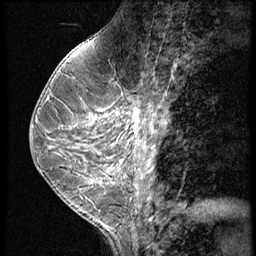
Breast MRI (dynamic contrast-enhanced), one sagittal slice; position 26 of 60 along the scan axis; 3 images stored at this slice position (order not interpretable as contrast timing); 1.5 T; TE 4.2 ms, TR 9 ms; 2.5 mm slice thickness; 256 × 256 image matrix, field of view 180 × 180 mm. Female patient, age 38 years. From the clinical record (not read from this slice): setting: breast cancer imaged before/during neoadjuvant chemotherapy; receptor status: triple-negative.
Annotated regions visible in this slice (semi-automatically segmented with operator editing):
- analysis volume of interest (the breast-tissue region the enhancement analysis was run in; not a lesion): bounding box <119,93,165,150> (left, top, right, bottom; pixels)
- tumour enhancement mask (voxels above the 140 % enhancement threshold inside the analysis volume of interest): <158,105,160,108>